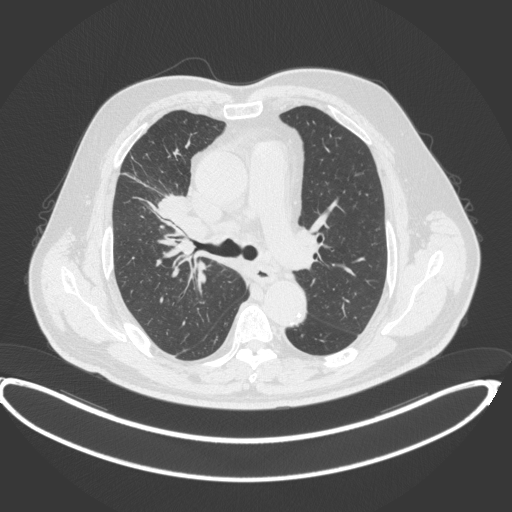
Chest CT, one axial slice; position 264 of 395 along the scan axis; reconstruction kernel B31f; lung window (W 1500 / L -600 HU); 1 mm slice thickness; 512 × 512 image matrix, field of view 448 × 448 mm. Patient: male, 62 years. Case-level facts recorded for this patient, not image findings: clinical TNM (as recorded): T1c N3 M1c.
Structures marked on this image (bounding box drawn by a radiologist):
- lung tumour (recorded histology: adenocarcinoma): bounding box <151,192,190,219> (left, top, right, bottom; pixels)